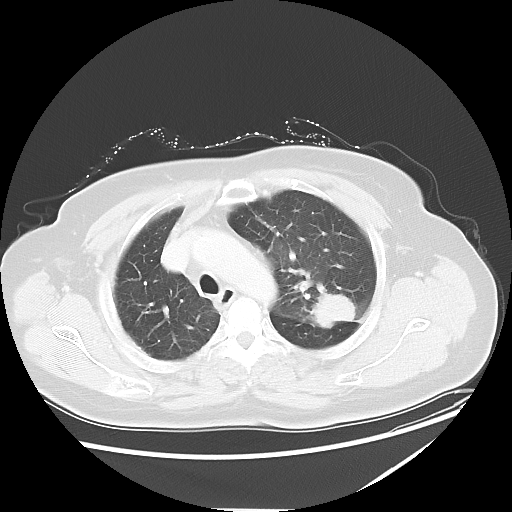
Chest CT, one axial slice; position 41 of 54 along the scan axis; reconstruction kernel LUNG; 120 kVp; lung window (W 1500 / L -600 HU); 5 mm slice thickness; 512 × 512 image matrix. Female patient, age 61 years. Case-level facts recorded for this patient, not image findings: clinical TNM (as recorded): T1c N3 M1.
Annotated regions visible in this slice (bounding box drawn by a radiologist):
- lung tumour (recorded histology: adenocarcinoma): bounding box (x1, y1, x2, y2) in pixels: (307, 288, 362, 328)